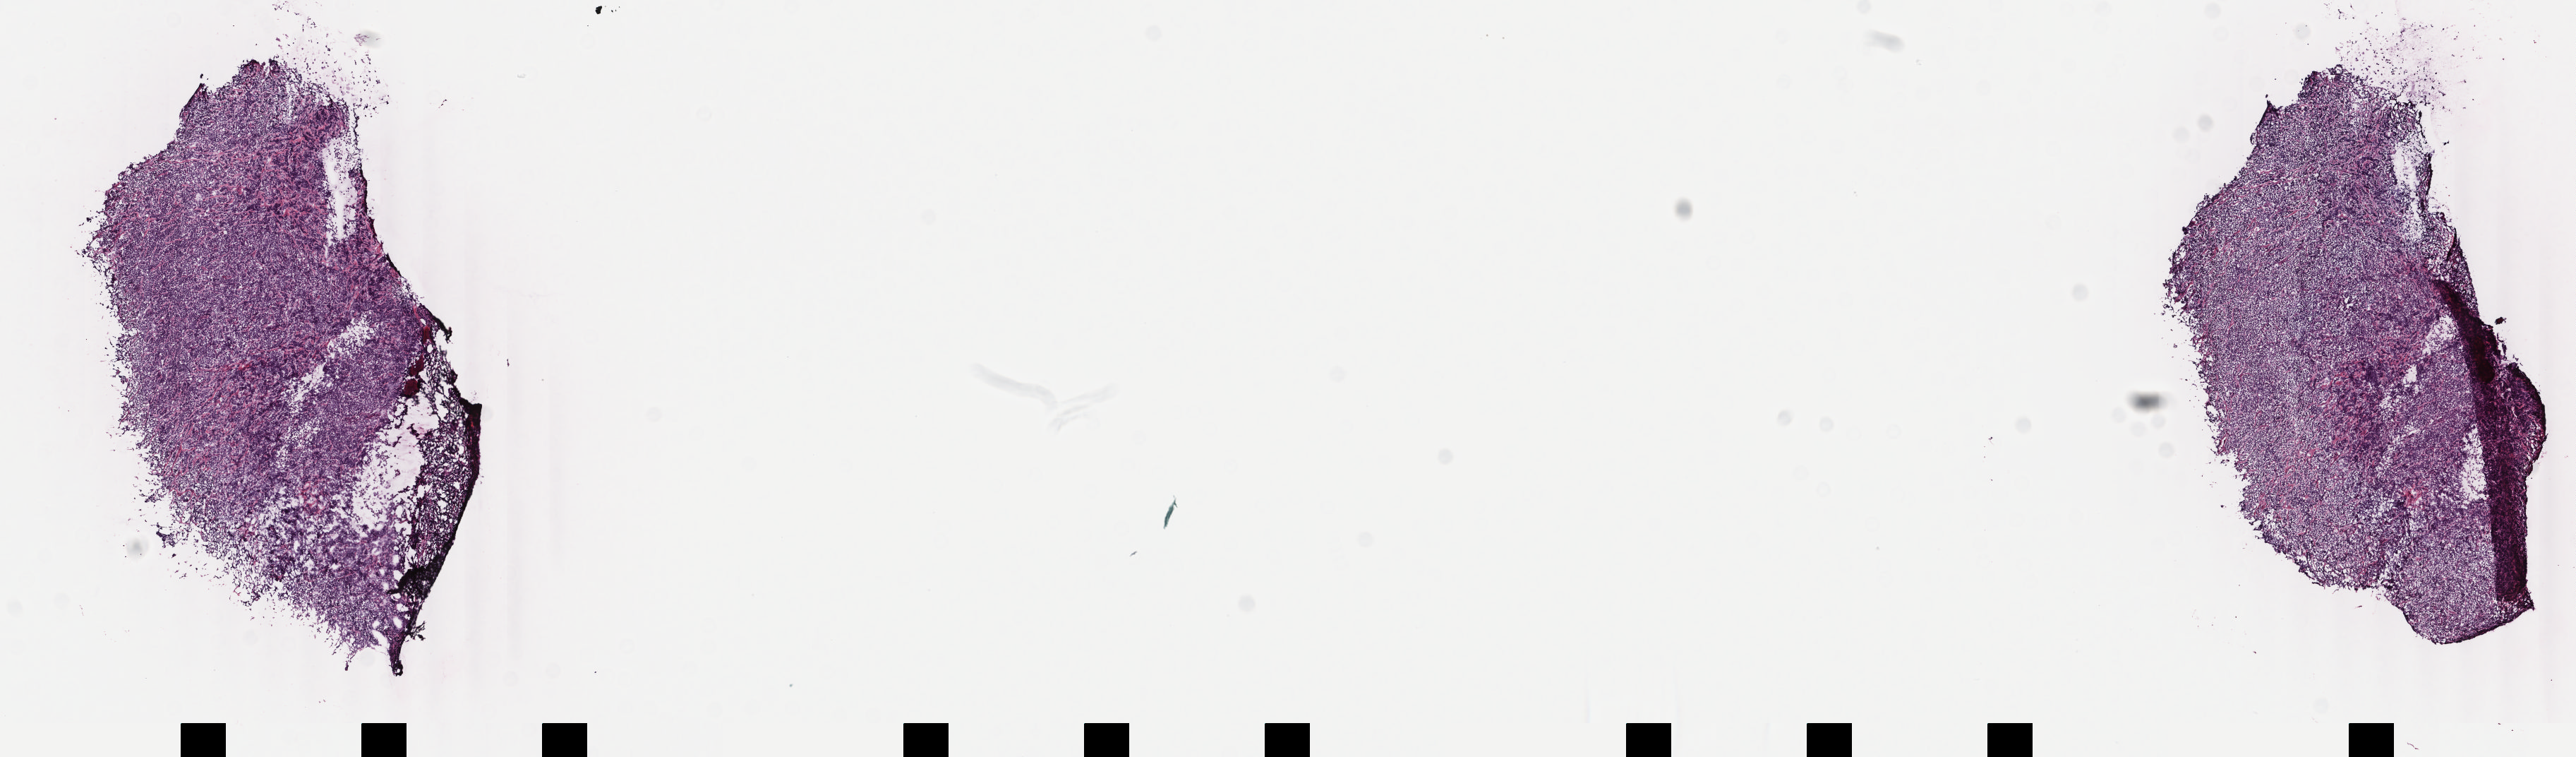
Digitized haematoxylin and eosin-stained section — a low-resolution overview of the entire scanned area, about 14.5 x 4.3 mm. Frozen section (tissue freezing medium). Specimen: primary tumor. Site: cranium. Male patient; age at initial diagnosis 5 years. Pathologist review of this section (percent, as recorded): tumor cells 85%, tumor nuclei 90%, stromal cells 10%, necrosis 5%, normal cells 0%. Infiltration values recorded for this section: lymphocyte infiltration 50%, monocyte infiltration 20%, neutrophil infiltration 10%.
Diagnosis: Burkitt lymphoma, NOS. Ann Arbor stage (patient): Stage II. Section: bottom of the tissue portion.